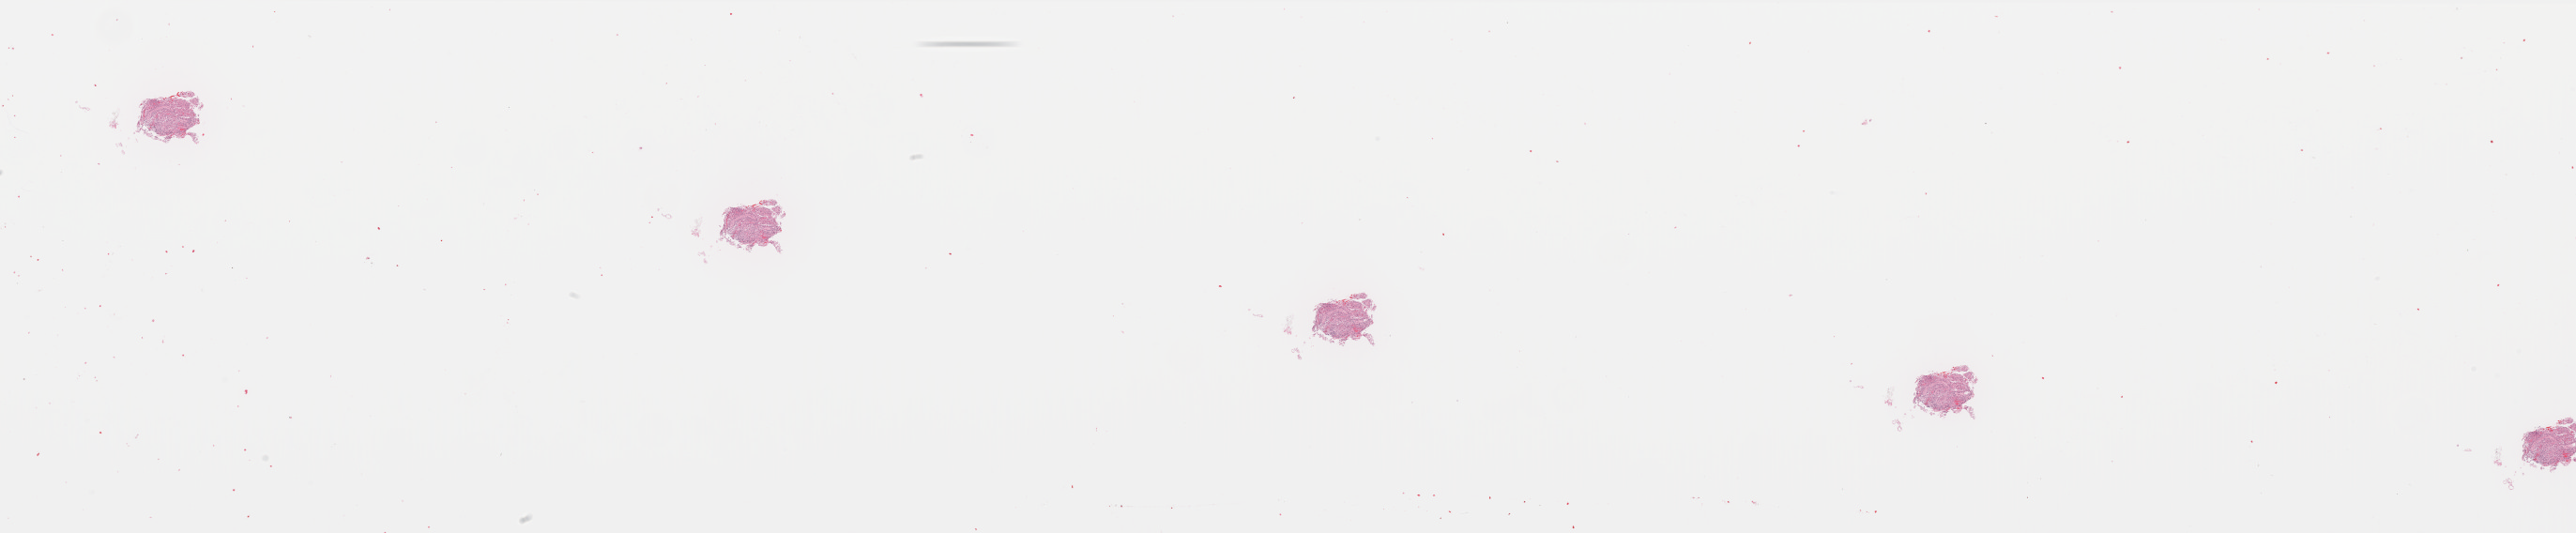
Digitized Hematoxylin and eosin (H&E) stained tissue section (whole slide), shown as a low-resolution overview of the whole scanned area (about 44.0 x 9.1 mm, from a 40x scan), FFPE section, sample: primary tumour, brain. Female, age 41 years at initial diagnosis. Histologic grade: G2 (moderately differentiated).
Laterality: right. Histologic diagnosis: Astrocytoma, NOS (cerebrum).